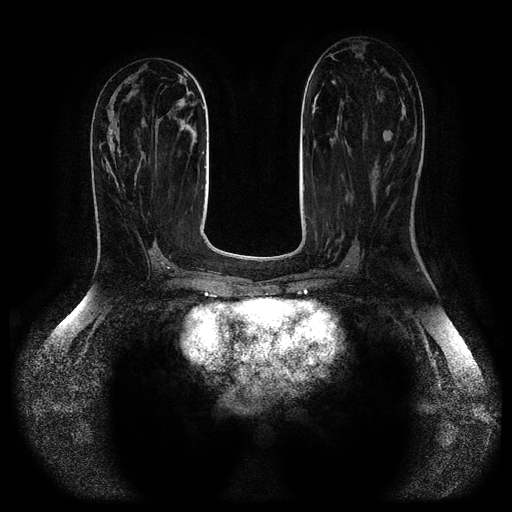
Breast MRI (dynamic contrast-enhanced, multi-phase), one axial slice. Position 41 of 116 along the scan axis. Dynamic contrast-enhanced series, time point 2 of 5 at this slice position (early post-contrast). 1.5 T. TE 2.6 ms, TR 5.2 ms. 2 mm slice thickness. 512 × 512 image matrix, field of view 380 × 380 mm. Patient: female, 44 years.
Annotated regions visible in this slice (semi-automatically segmented with operator editing):
- breast lesion (labelled benign in the annotation): bounding box (x1, y1, x2, y2) in pixels: (383, 133, 390, 143)